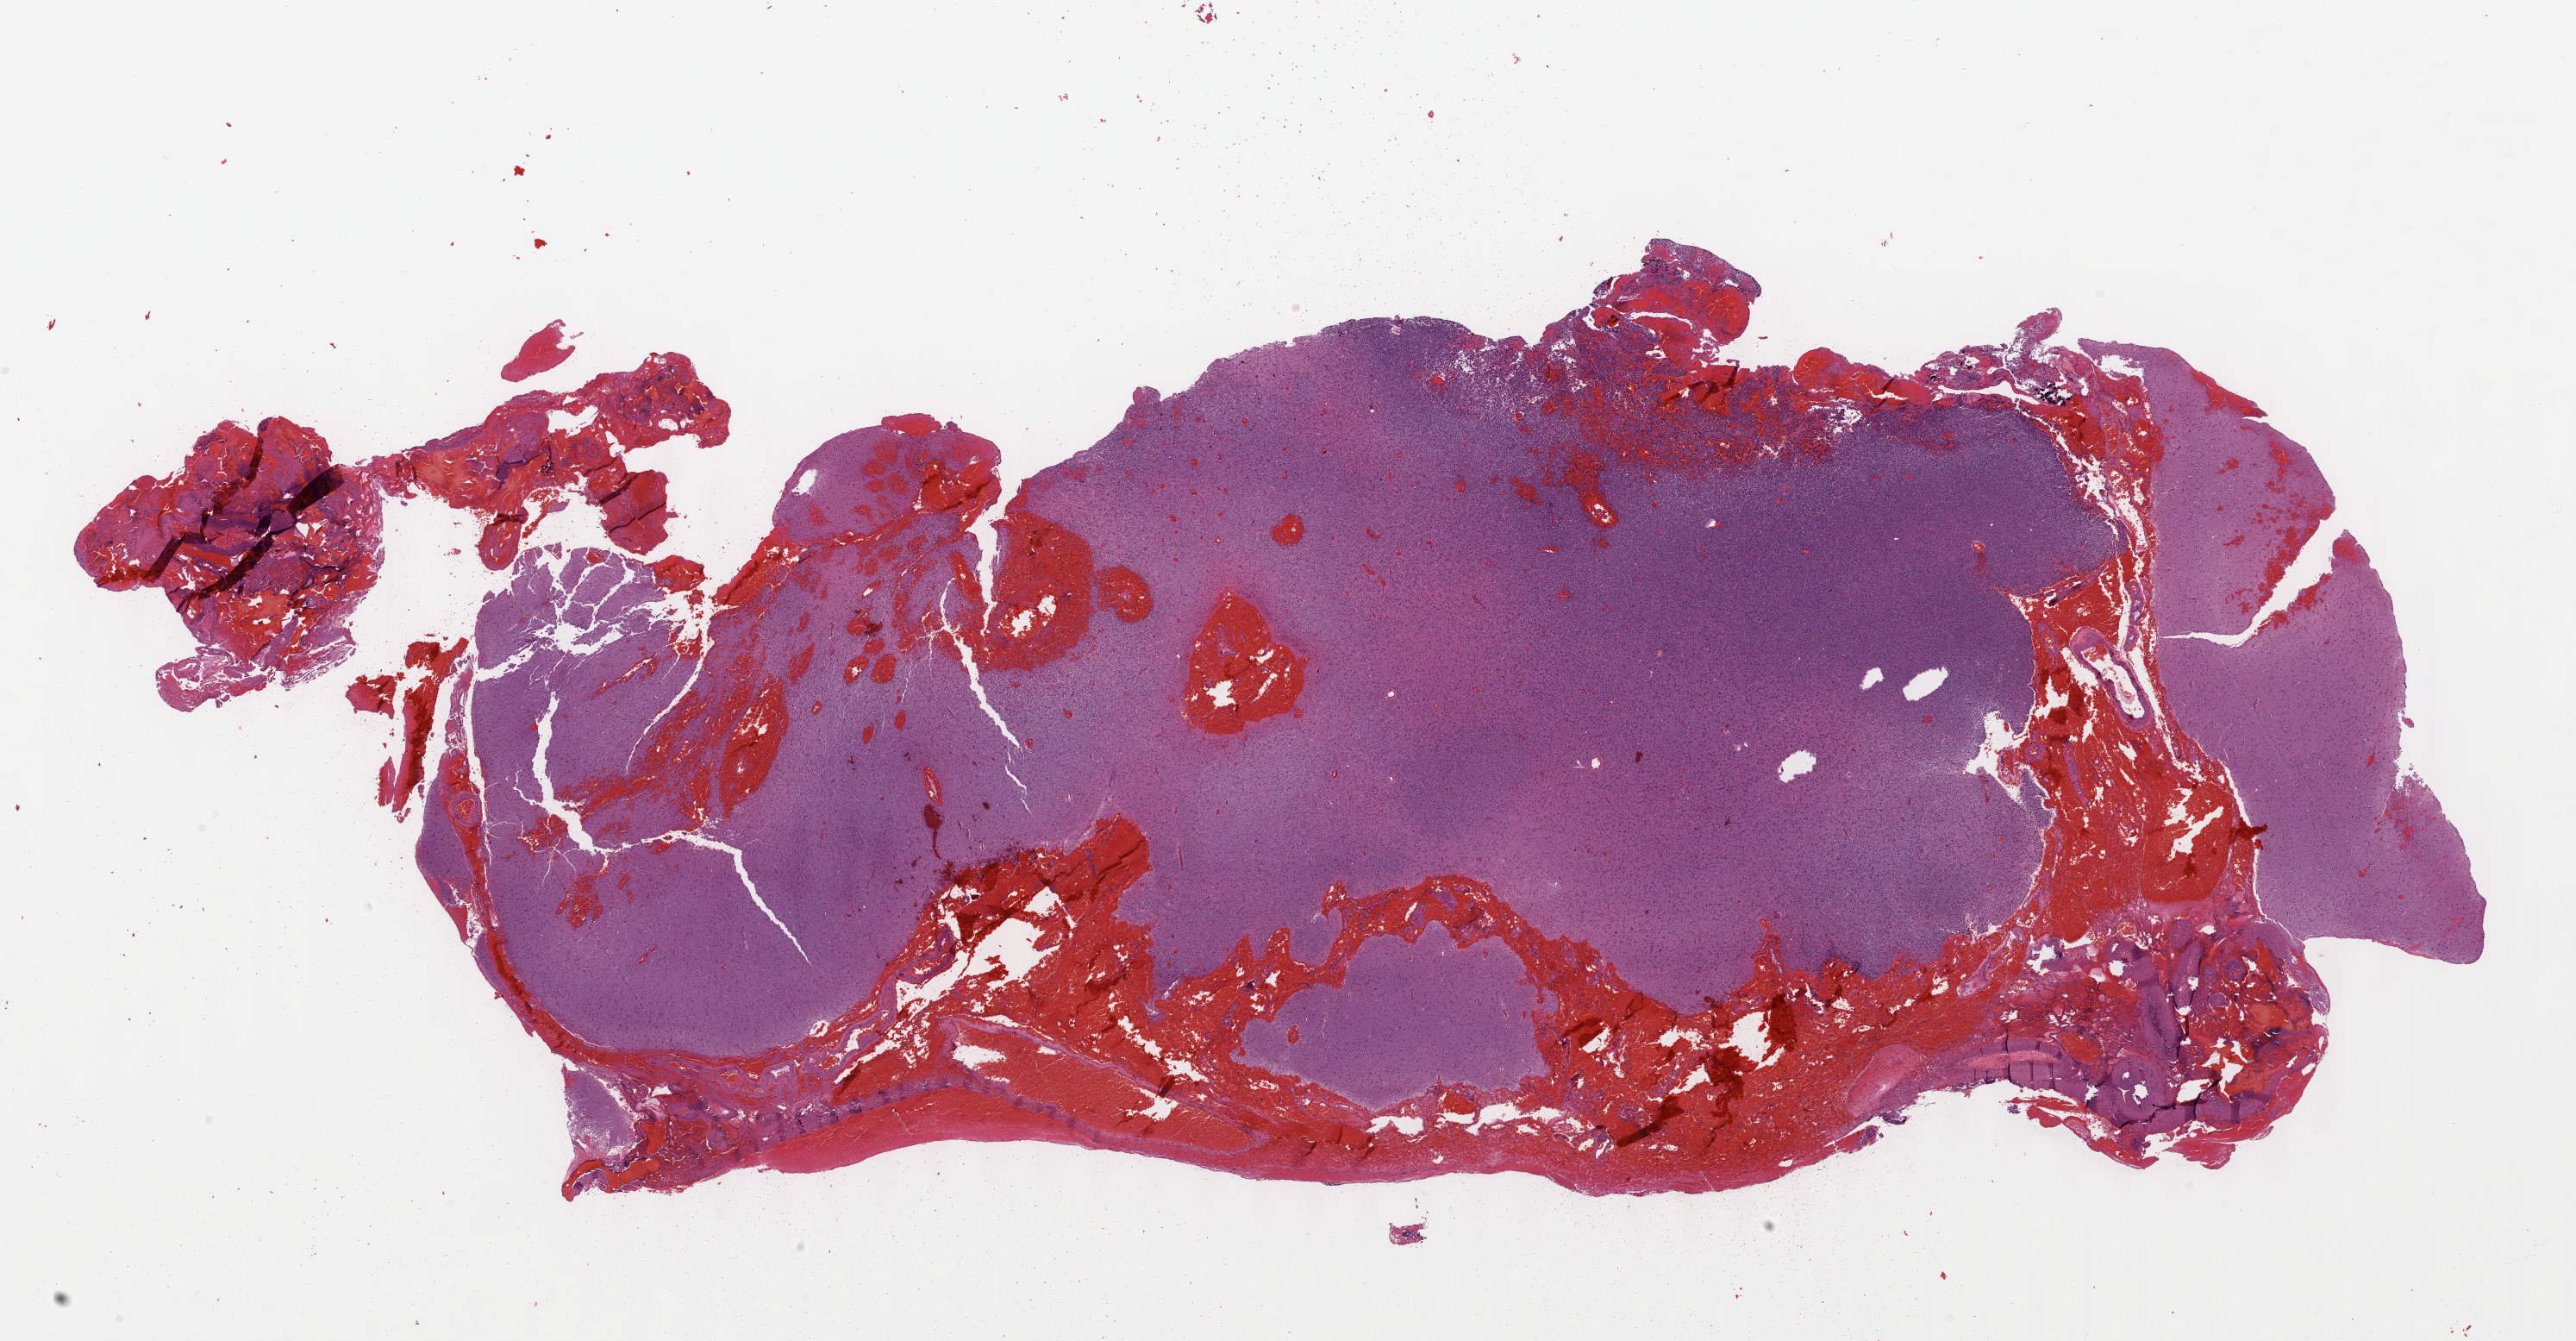
Whole-slide histology image, H&E, low-resolution overview of the scanned area, about 24.1 x 12.6 mm; formalin-fixed paraffin-embedded (FFPE) diagnostic section; primary tumour sample from the brain. Female, age 51 years at initial diagnosis. Histologic grade: G3 (poorly differentiated).
Pathologic diagnosis: Oligodendroglioma, anaplastic (cerebrum). Laterality: left.